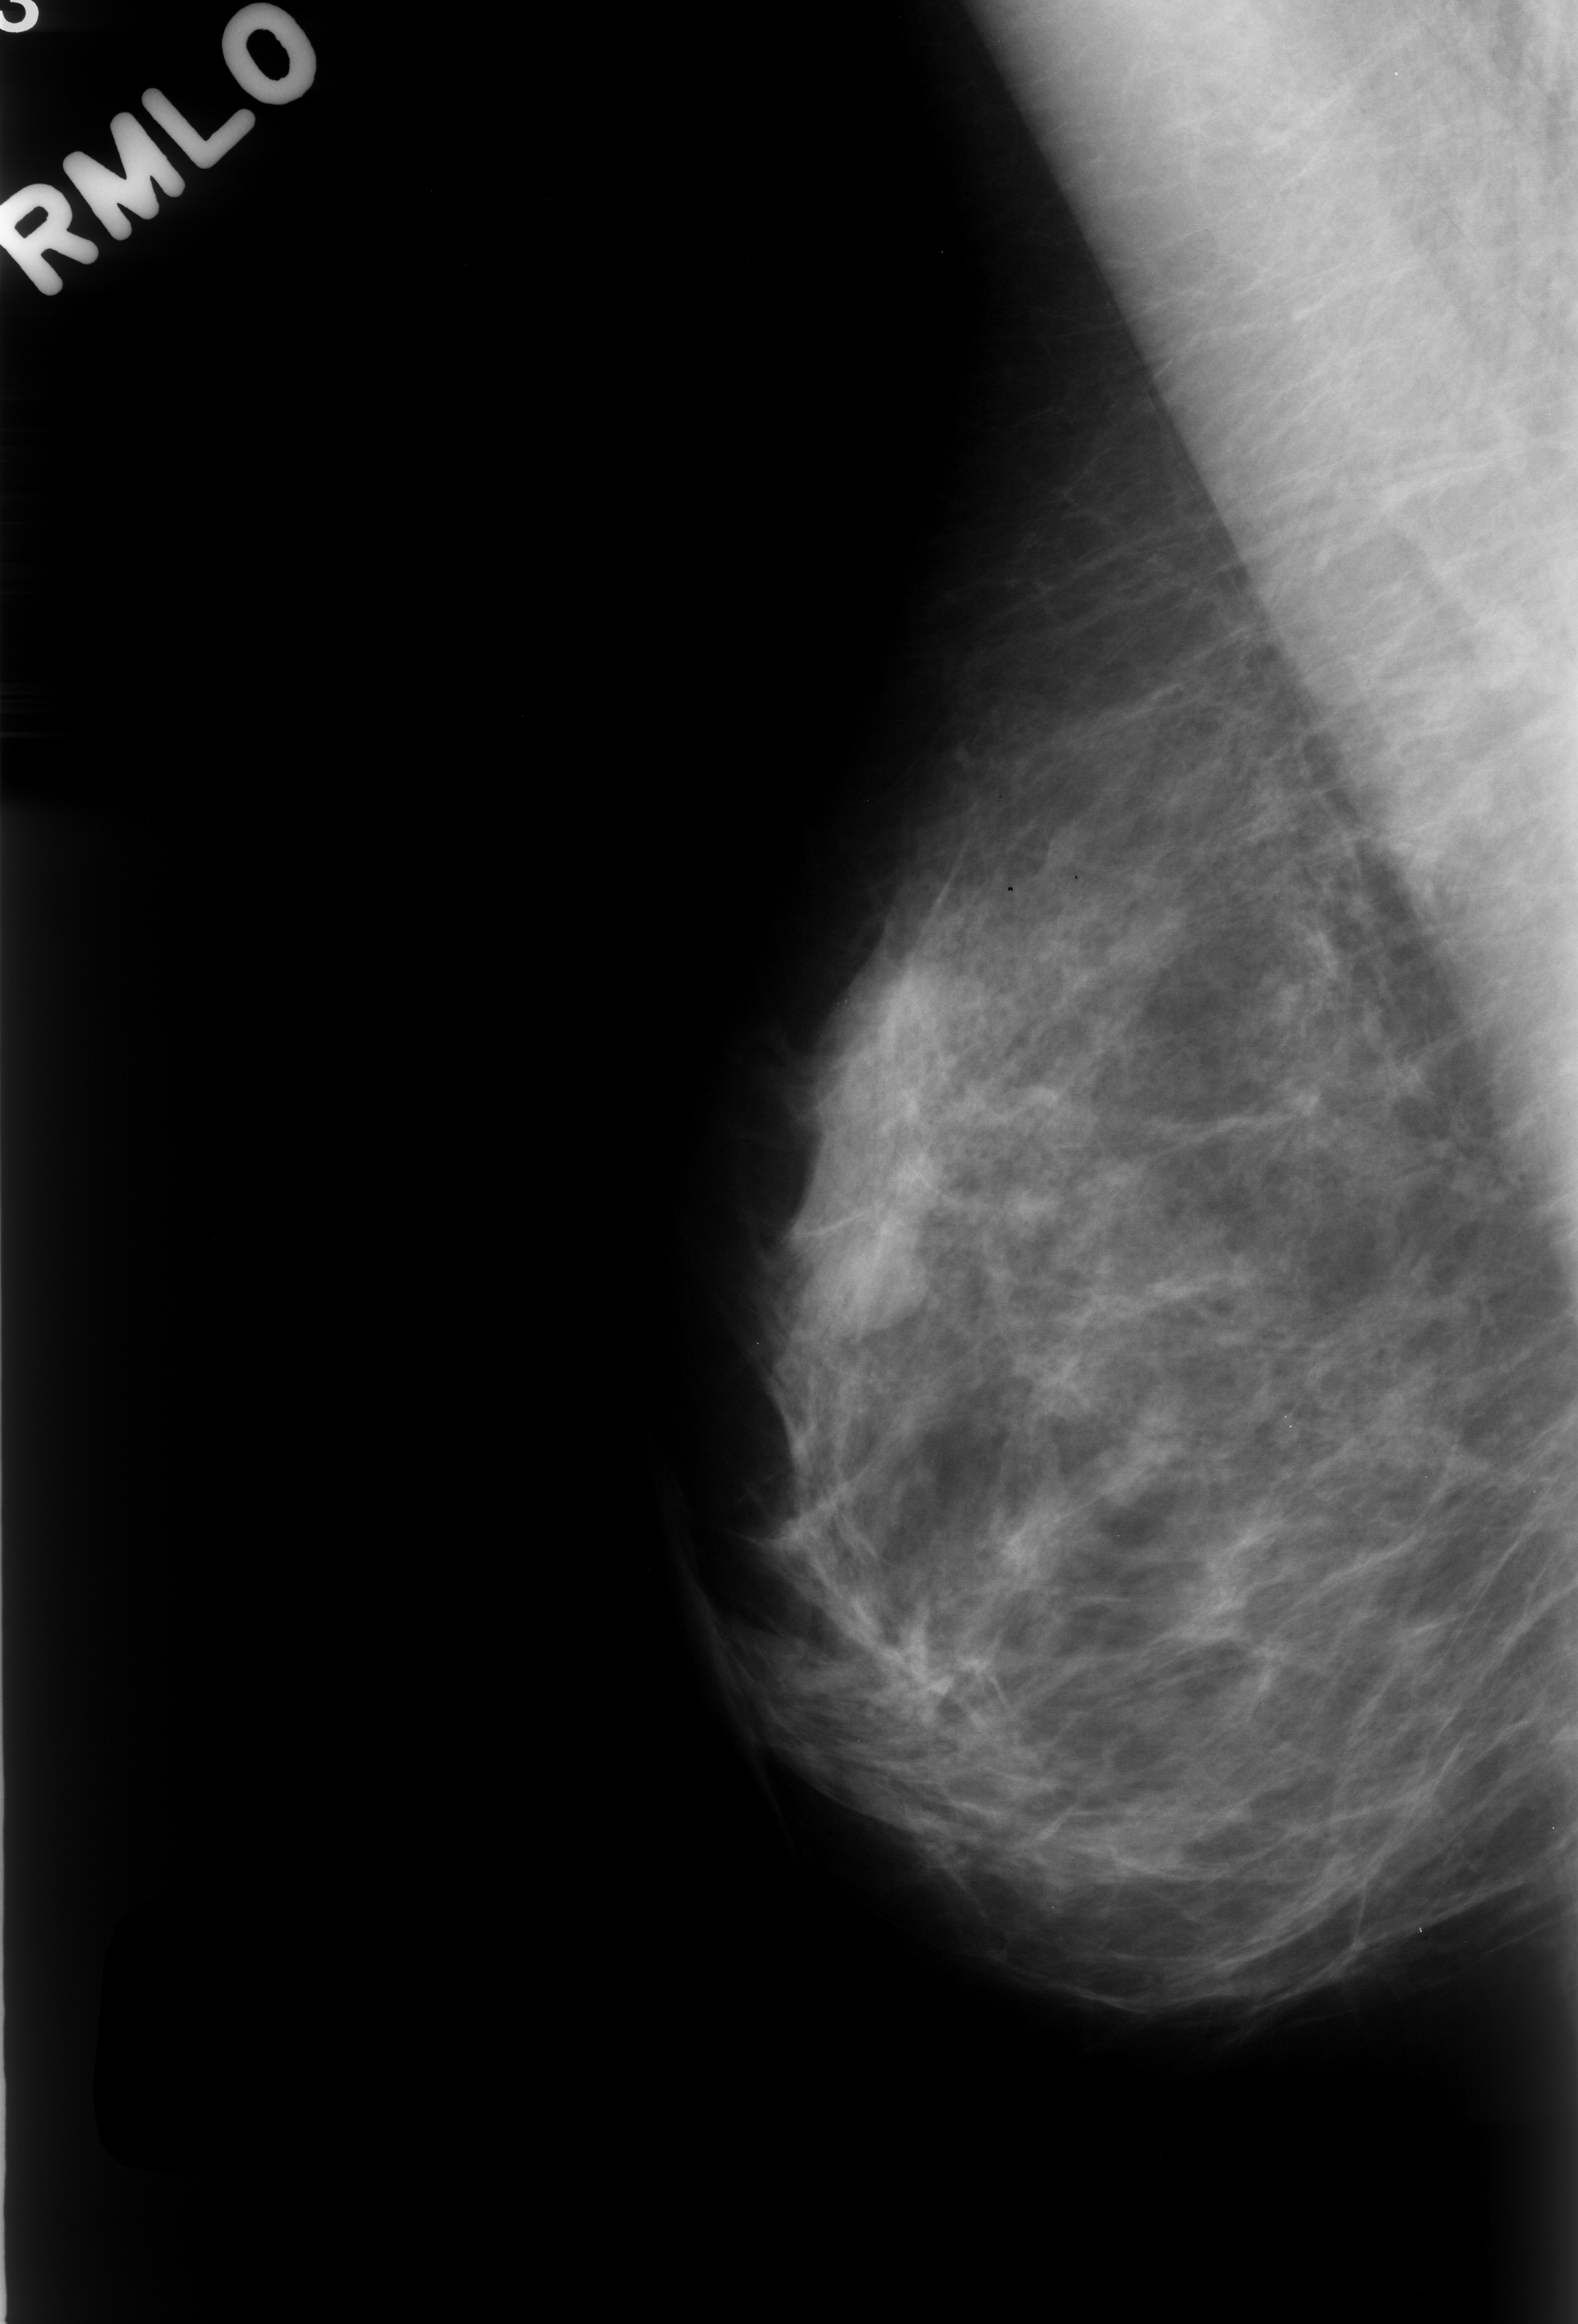
Digitized screen-film mammogram; right breast; mediolateral oblique (MLO) view; breast composition: scattered fibroglandular densities (BI-RADS density category 2 of 4).
Marked findings (only marked abnormalities are described; nothing is implied about the rest of the image): mass, shape oval, margins circumscribed; BI-RADS assessment category 3; pathology (as recorded): benign.